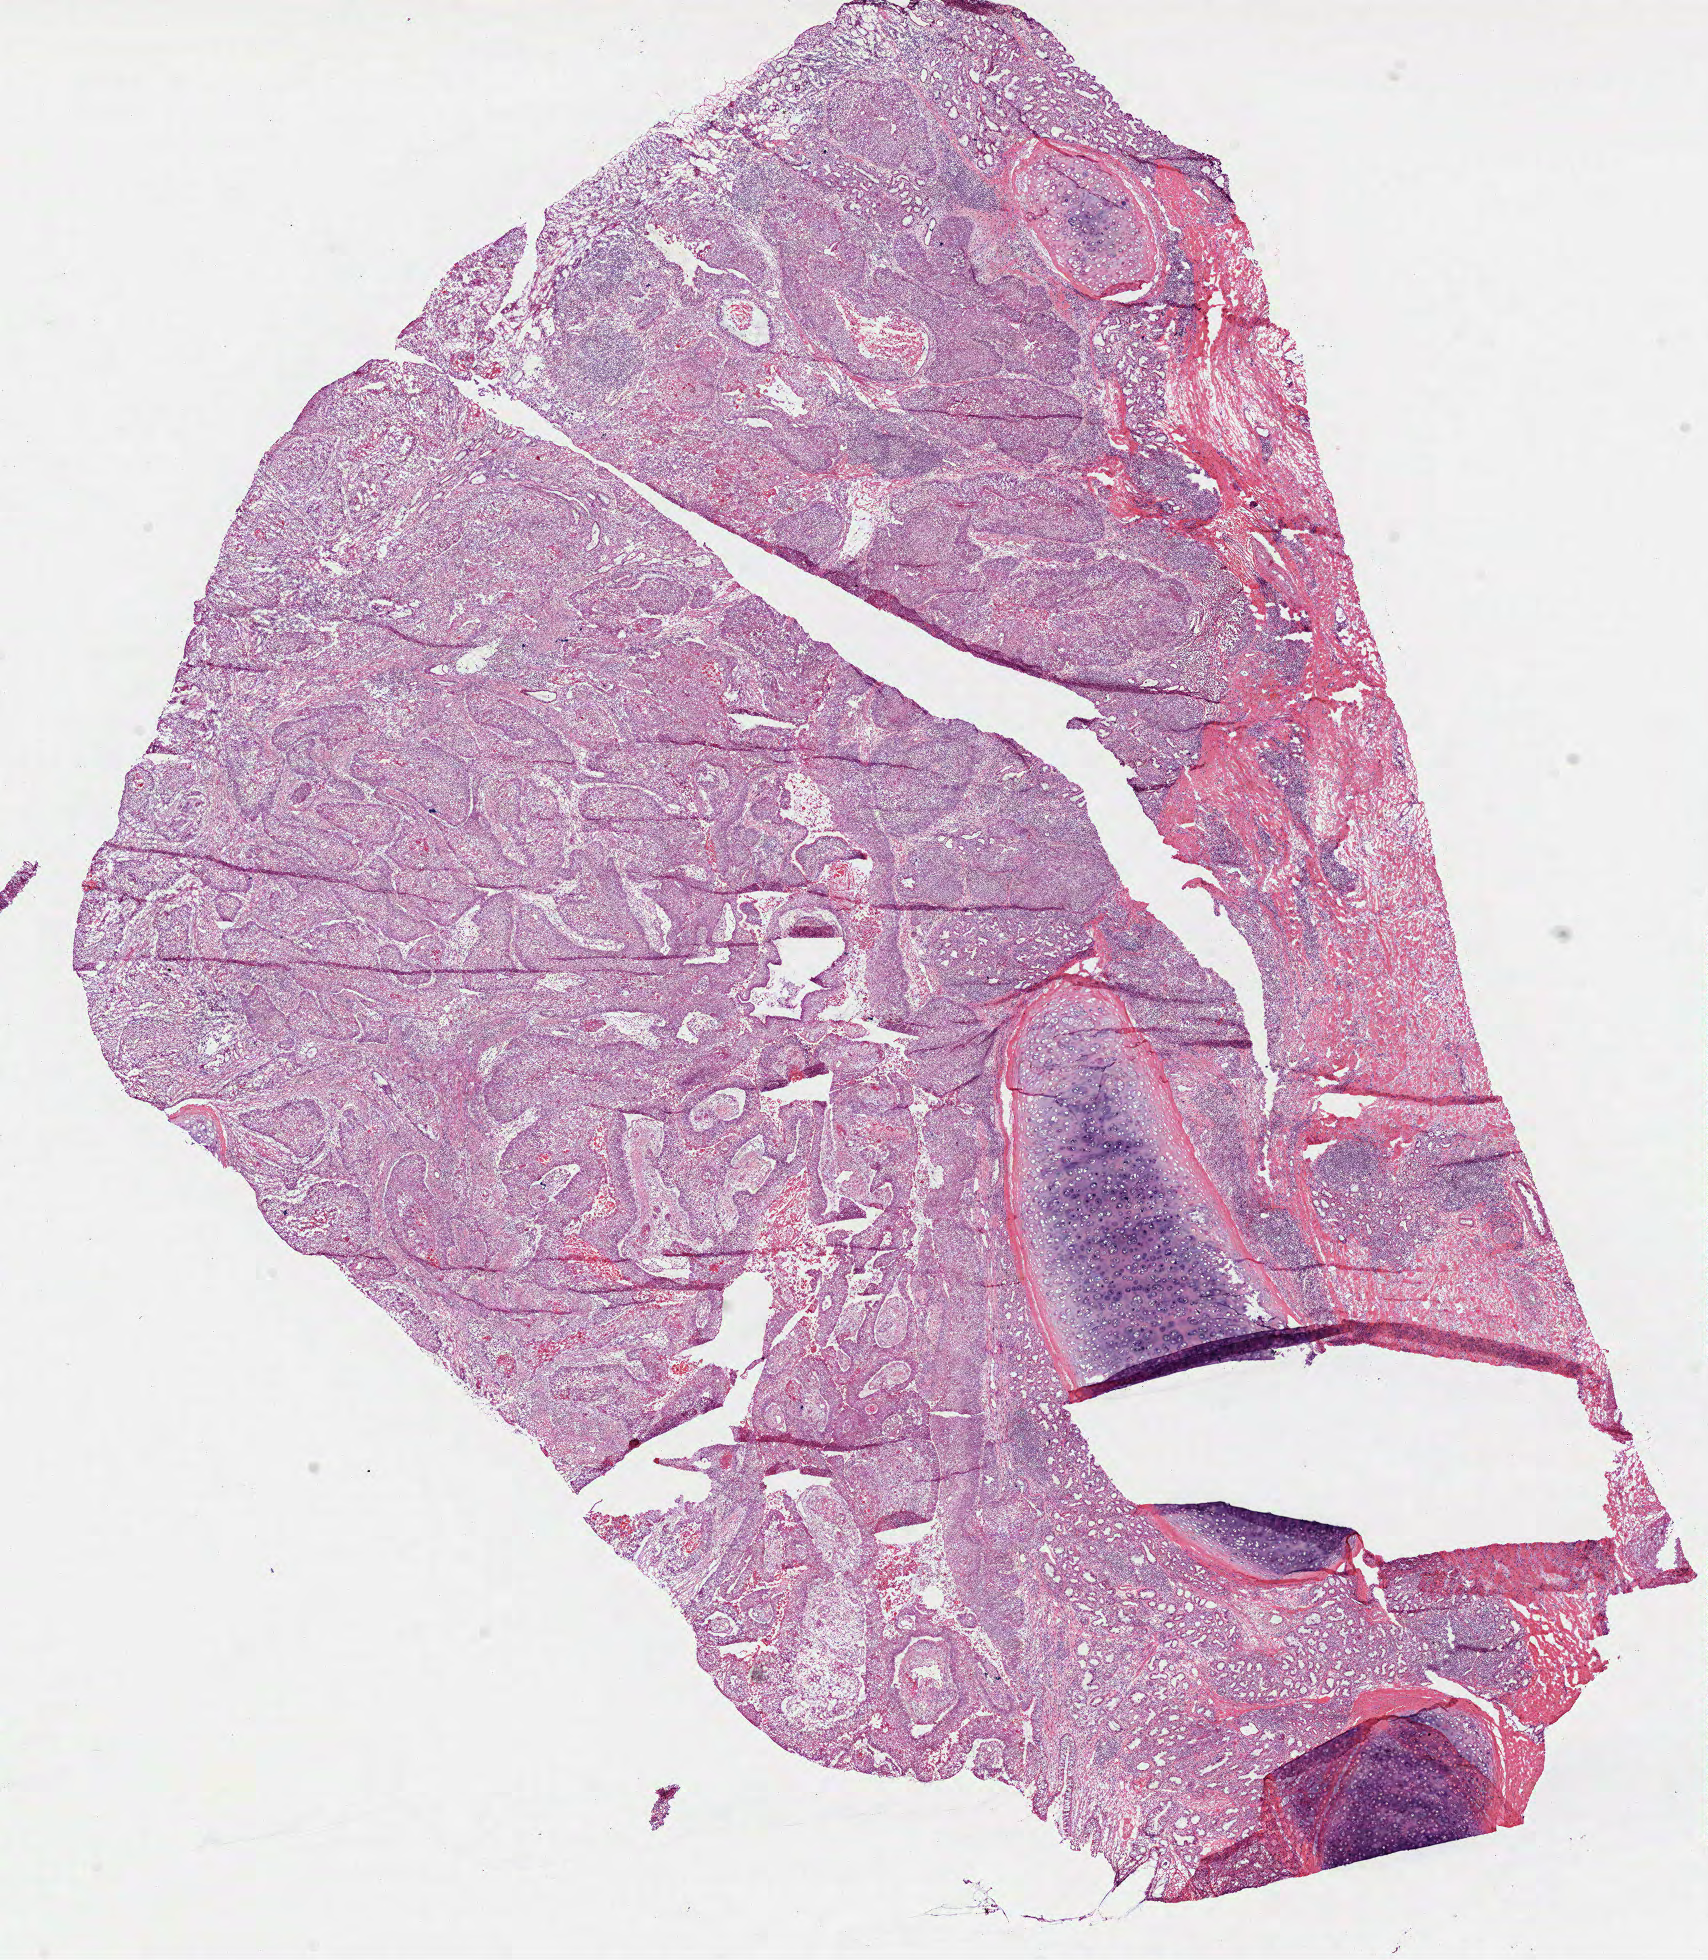
Digitized Hematoxylin and eosin (H&E) stained tissue section (whole slide) — a low-resolution overview of the entire scanned area, about 13.8 x 15.8 mm (from a 40x scan). Frozen section from the top of the tissue portion. Primary tumour sample from the lung. Male patient; age at initial diagnosis 49 years. Slide review estimates, as recorded: tumour cells 60%, tumour nuclei 62%.
Diagnosis: Squamous cell carcinoma, NOS.